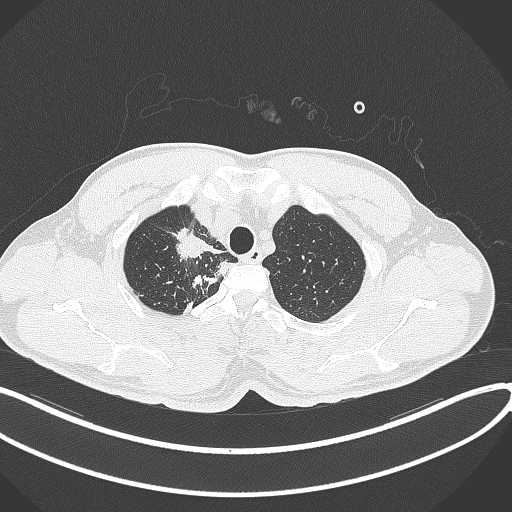
Chest CT, one axial slice. Slice 327 of 391 in the series (ordered by position). Reconstruction kernel B70f. 120 kVp. Lung window (W 1500 / L -600 HU). 512 × 512 image matrix, field of view 400 × 400 mm. Male patient, age 48 years. From the clinical record (not read from this slice): clinical TNM (as recorded): T1c N1 M1.
Annotated regions visible in this slice (rectangle marked by the reading radiologist):
- lung tumour (recorded histology: adenocarcinoma): bounding box [x1, y1, x2, y2] px = [171, 228, 207, 262]